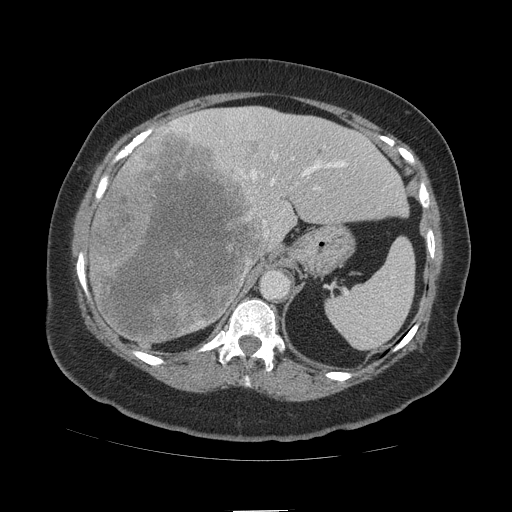
Contrast-enhanced abdominal CT (liver protocol), one axial slice; slice 76 of 109 in the series (ordered by position); reconstruction kernel STANDARD; soft-tissue window (W 400 / L 40 HU); 2.5 mm slice thickness; 512 × 512 image matrix. From the clinical record (not read from this slice): diagnosis: hepatocellular carcinoma (patient treated with transarterial chemoembolisation; whether this scan precedes or follows treatment is not stated here); TNM stage (as recorded): Stage-IVB; Child-Pugh class: A; tumour nodularity: multinodular.
Annotated regions visible in this slice (semi-automatic segmentation, software-assisted and operator-edited):
- liver parenchyma outside the tumour (the mass and vessels are separate outlines, so this box may not span the whole liver): box from (x=88, y=106) to (x=406, y=343) px
- mass: (x=90, y=132)–(x=273, y=349)
- liver vessels: (x=166, y=109)–(x=348, y=189)